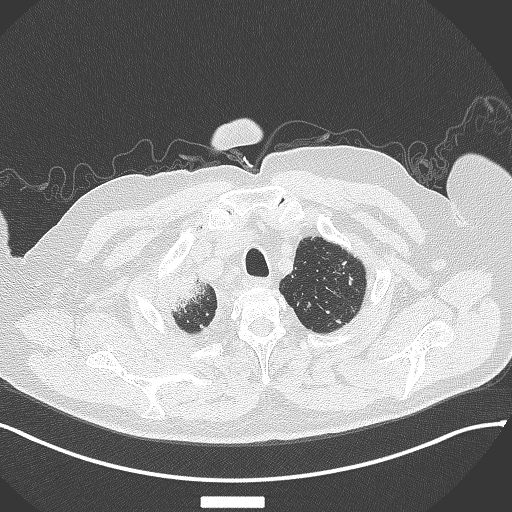
Chest CT, one axial slice. Slice 331 of 384 in the series (ordered by position). Reconstruction kernel B70f. Lung window (W 1500 / L -600 HU). 1 mm slice thickness. 512 × 512 image matrix, field of view 400 × 400 mm. Male patient, age 69 years. From the clinical record (not read from this slice): clinical TNM (as recorded): T4 N3 M1.
Structures marked on this image (bounding box drawn by a radiologist):
- lung tumour (recorded histology: adenocarcinoma): bounding box <166,268,215,314> (left, top, right, bottom; pixels)